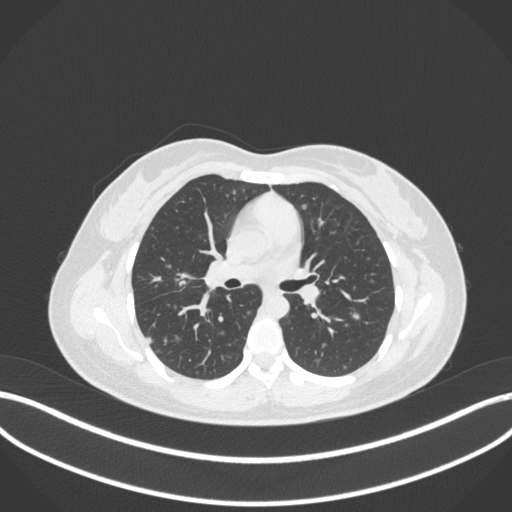
Chest CT, one axial slice. Position 193 of 214 along the scan axis. 120 kVp. Lung window (W 1500 / L -600 HU). 1 mm slice thickness. 512 × 512 image matrix, field of view 400 × 400 mm. Patient: female, 33 years. From the clinical record (not read from this slice): clinical TNM (as recorded): T1c N0 M0; histopathological grade: G2-G3.
Annotated regions visible in this slice (rectangle marked by the reading radiologist):
- lung tumour (recorded histology: adenocarcinoma): bounding box (x1, y1, x2, y2) in pixels: (171, 271, 196, 291)